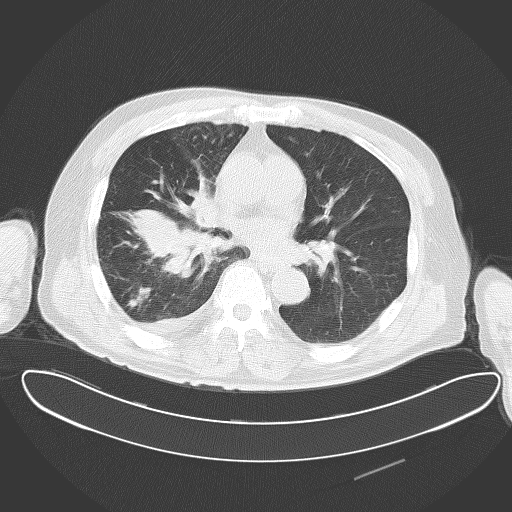
Chest CT, one axial slice. Position 29 of 62 along the scan axis. Lung window (W 1500 / L -600 HU). 5 mm slice thickness. 512 × 512 image matrix. Male patient, age 78 years. From the clinical record (not read from this slice): clinical TNM (as recorded): T2 N1 M1.
Outlined on this slice (rectangle marked by the reading radiologist):
- lung tumour (recorded histology: adenocarcinoma): bounding box <125,181,224,275> (left, top, right, bottom; pixels)